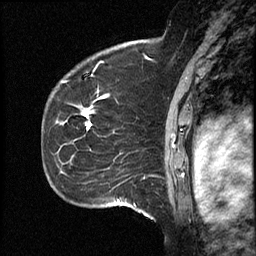
Breast MRI (dynamic contrast-enhanced), one sagittal slice; position 34 of 46 along the scan axis; dynamic contrast-enhanced study with each time point stored as its own series, time point 2 of 4 at this slice position (early post-contrast, ordered by acquisition time); 1.5 T; TE 4.2 ms, TR 18.3 ms; 3 mm slice thickness; 256 × 256 image matrix. Case-level facts recorded for this patient, not image findings: setting: breast cancer imaged before/during neoadjuvant chemotherapy; receptor status: HR-positive, HER2-negative.
Outlined on this slice (semi-automatically segmented with operator editing):
- analysis volume of interest (the breast-tissue region the enhancement analysis was run in; not a lesion): bounding box (x1, y1, x2, y2) in pixels: (64, 72, 111, 209)
- tumour enhancement mask (voxels above the 100 % enhancement threshold inside the analysis volume of interest): (82, 111, 90, 128)